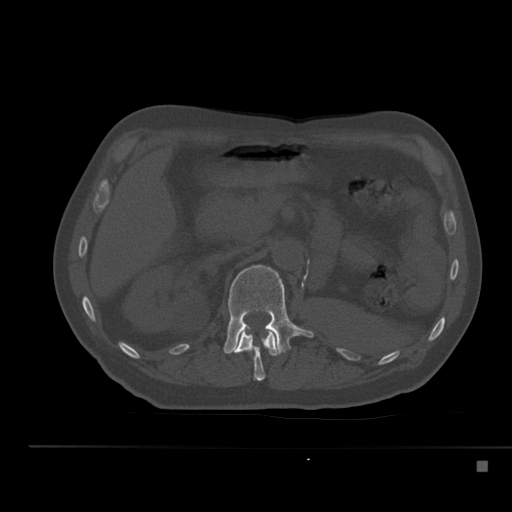
CT including the spine, one axial slice. Slice 214 of 517 in the series (ordered by position). Reconstruction kernel Br40s. Bone window (W 1800 / L 400 HU). 1.5 mm slice thickness. 512 × 512 image matrix, field of view 408 × 408 mm. Male patient, age 70 years. From the clinical record (not read from this slice): primary cancer: renal.
Structures marked on this image (semi-automatically segmented with operator editing):
- L1 vertebra: box from (x=223, y=265) to (x=313, y=355) px
- T12 vertebra: (x=231, y=329)–(x=279, y=381)